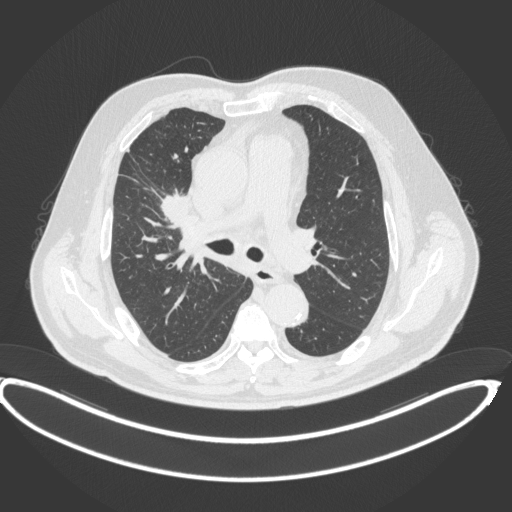
Chest CT, one axial slice; position 257 of 395 along the scan axis; reconstruction kernel B31f; lung window (W 1500 / L -600 HU); 1 mm slice thickness; 512 × 512 image matrix, field of view 448 × 448 mm. Patient: male, 62 years. From the clinical record (not read from this slice): clinical TNM (as recorded): T1c N3 M1c.
Outlined on this slice (bounding box drawn by a radiologist):
- lung tumour (recorded histology: adenocarcinoma): bounding box (x1, y1, x2, y2) in pixels: (157, 187, 195, 221)